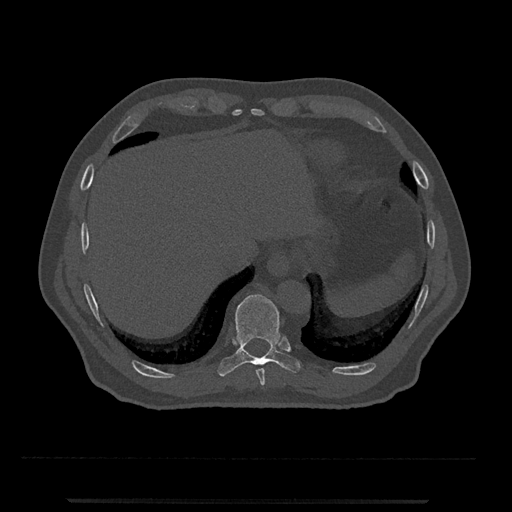
CT including the spine, one axial slice; position 530 of 797 along the scan axis; 120 kVp; bone window (W 1800 / L 400 HU); 0.5 mm slice thickness; 512 × 512 image matrix, field of view 419 × 419 mm. Male patient, age 63 years. Case-level facts recorded for this patient, not image findings: primary cancer: prostate.
Annotated regions visible in this slice (semi-automatic segmentation, software-assisted and operator-edited):
- T10 vertebra: bounding box [x1, y1, x2, y2] px = [217, 294, 301, 377]
- T9 vertebra: [256, 368, 265, 385]